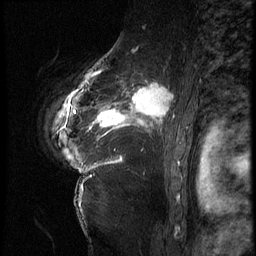
Breast MRI (dynamic contrast-enhanced), one sagittal slice. Position 49 of 62 along the scan axis. 3 images stored at this slice position (order not interpretable as contrast timing). 1.5 T. TE 4.2 ms, TR 9 ms. 2.5 mm slice thickness. 256 × 256 image matrix, field of view 180 × 180 mm. Patient: female, 56 years. Case-level facts recorded for this patient, not image findings: setting: breast cancer imaged before/during neoadjuvant chemotherapy; receptor status: HER2-positive.
Annotated regions visible in this slice (semi-automatically segmented with operator editing):
- analysis volume of interest (the breast-tissue region the enhancement analysis was run in; not a lesion): bounding box [x1, y1, x2, y2] px = [84, 75, 181, 153]
- tumour enhancement mask (voxels above the 140 % enhancement threshold inside the analysis volume of interest): [84, 75, 174, 138]